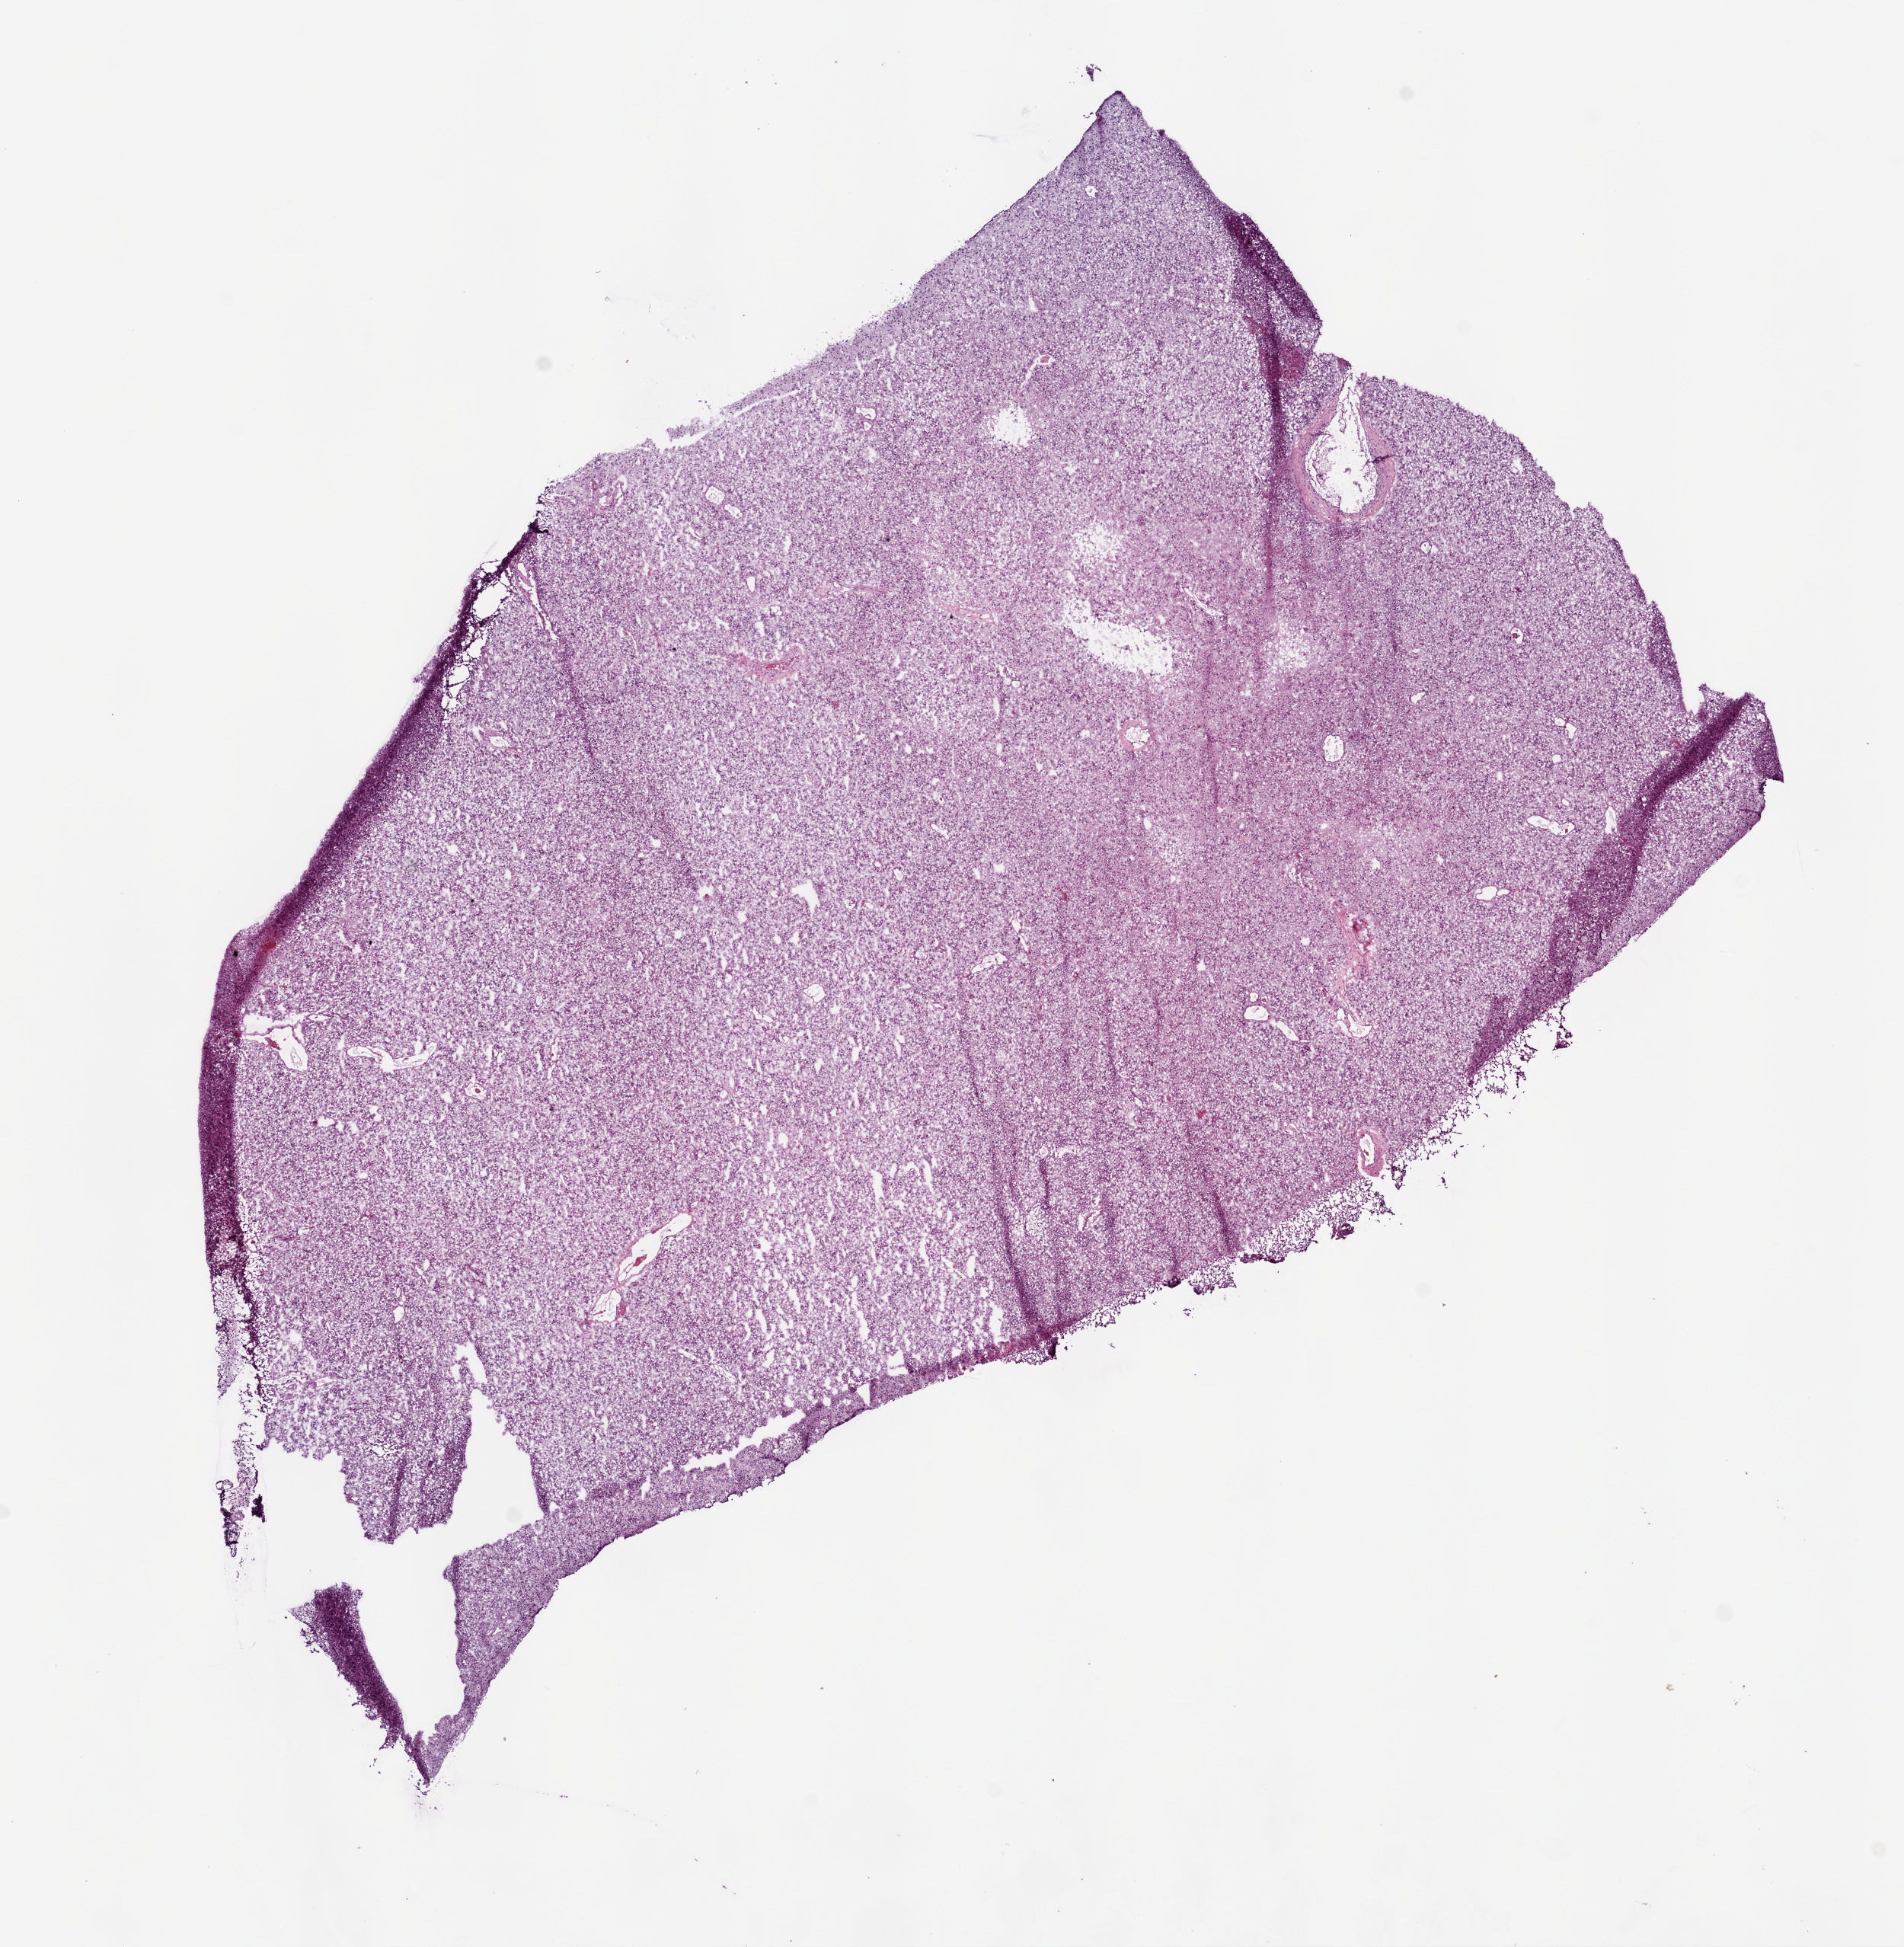
Whole-slide histology image, H&E-stained, a low-resolution overview of the entire scanned area, about 10.0 x 10.3 mm (from a 20x scan); frozen section; brain, primary tumour sample. Female patient; age at initial diagnosis 56 years. Composition of this section per pathologist review: tumour cells 90%, tumour nuclei 80%, normal cells 0%, stromal cells 0%, necrosis 10%.
Pathologic diagnosis: Glioblastoma.